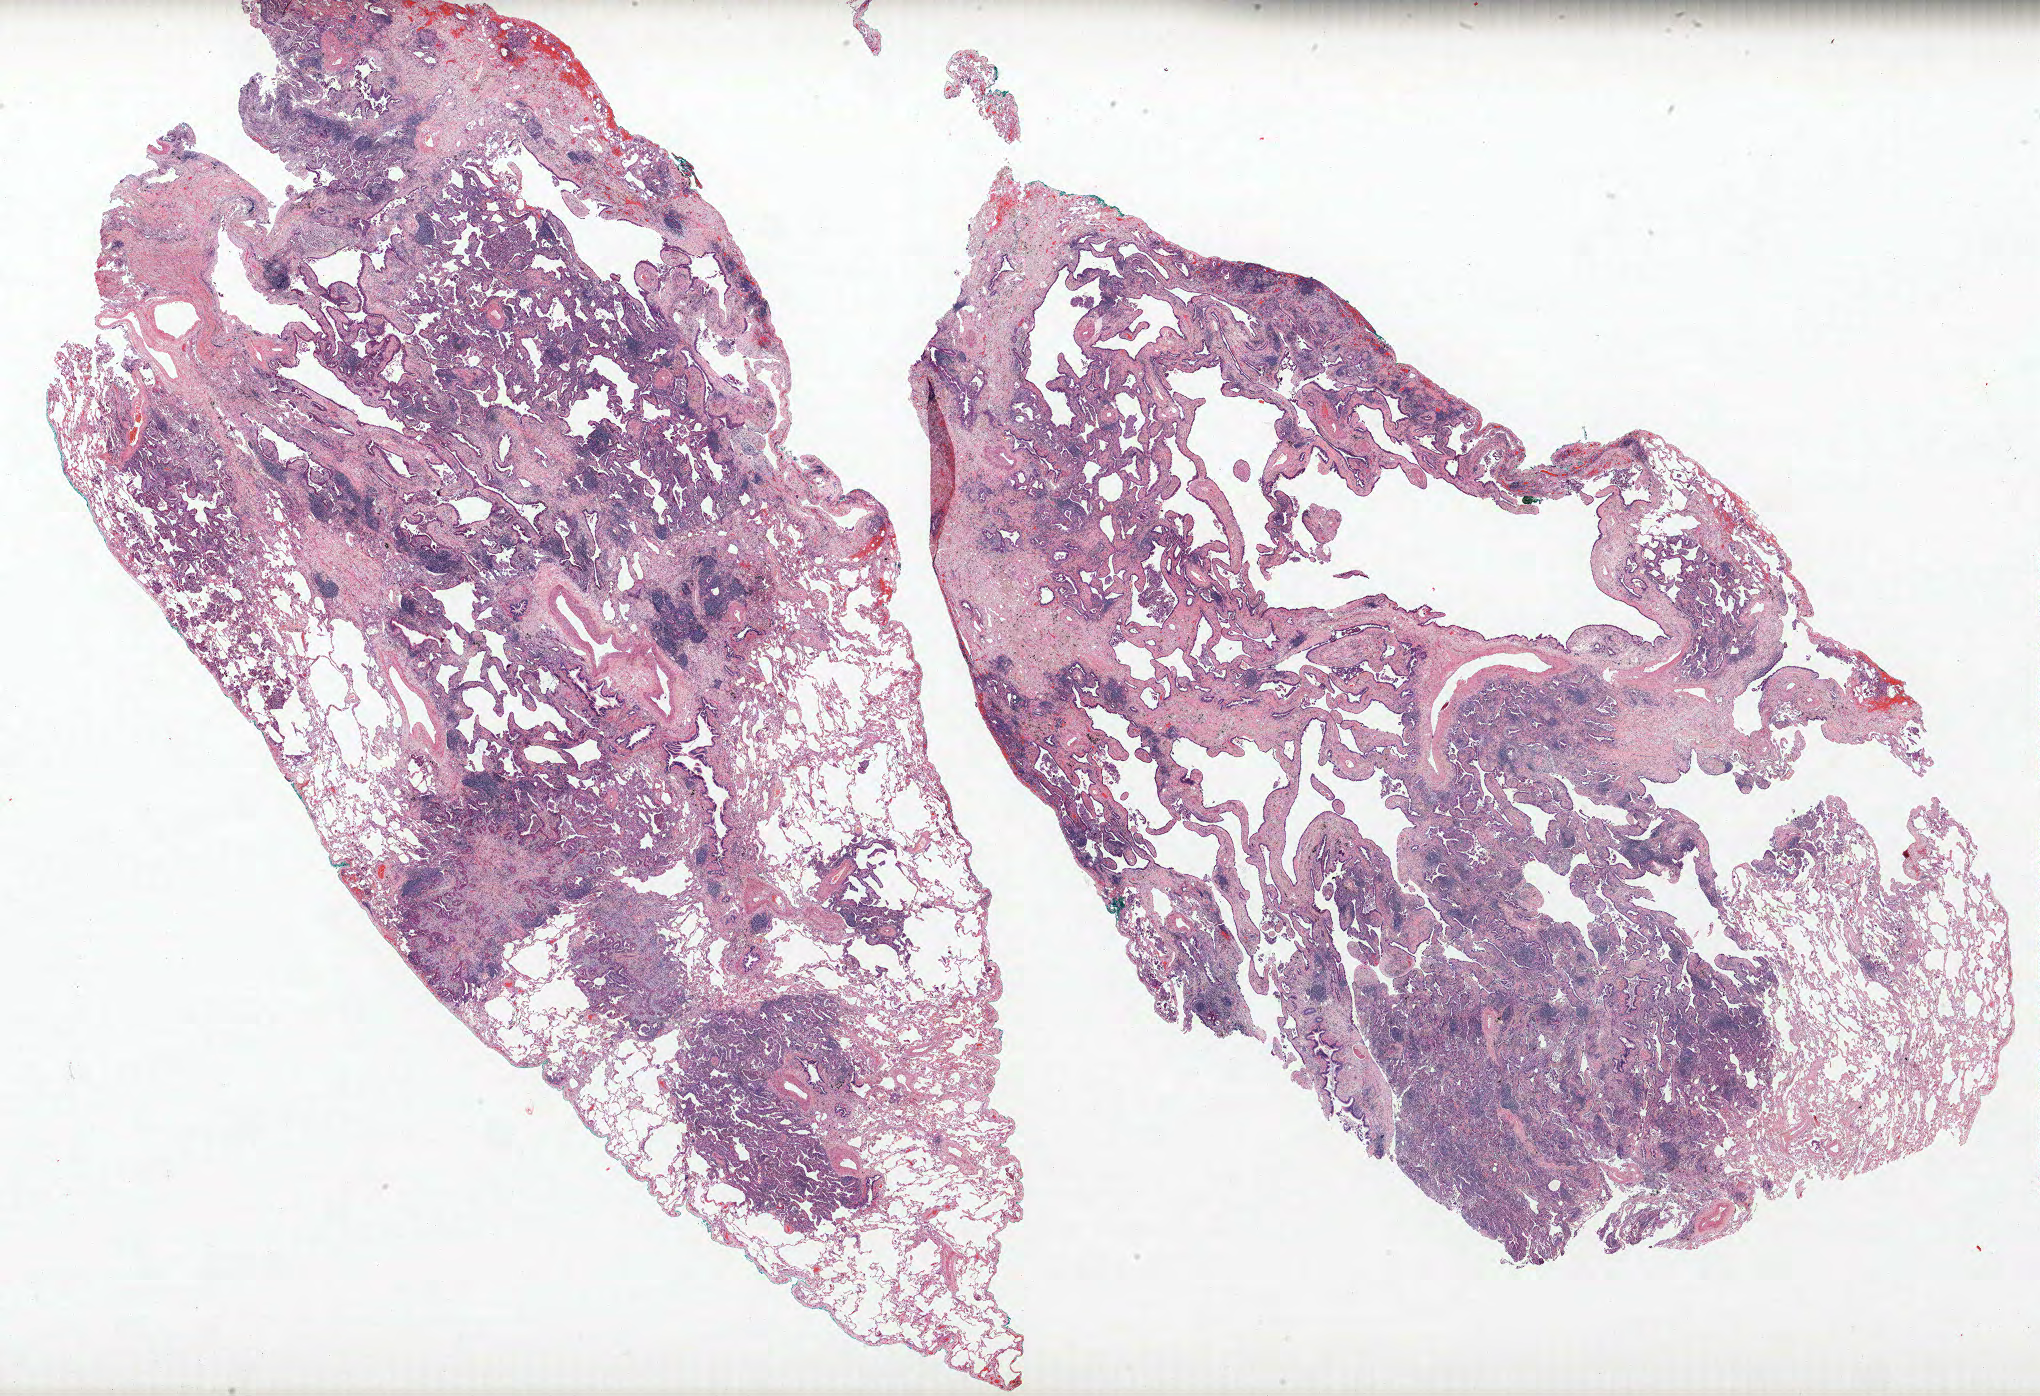
H&E whole-slide image, whole scanned area (about 32.6 x 22.3 mm, slide scanned at 40x) shown as a low-resolution overview, FFPE section, lung. Female, age 64 at enrolment. Grade: moderately differentiated (G2).
Stage (AJCC 6th edition): IA. Primary tumour location (clinical record): left lower lobe. Tumour size (pathology): 17 mm. ICD-O-3 topography: lower lobe of lung (C34.3). Participant's lung-cancer diagnosis: Adenocarcinoma, NOS.